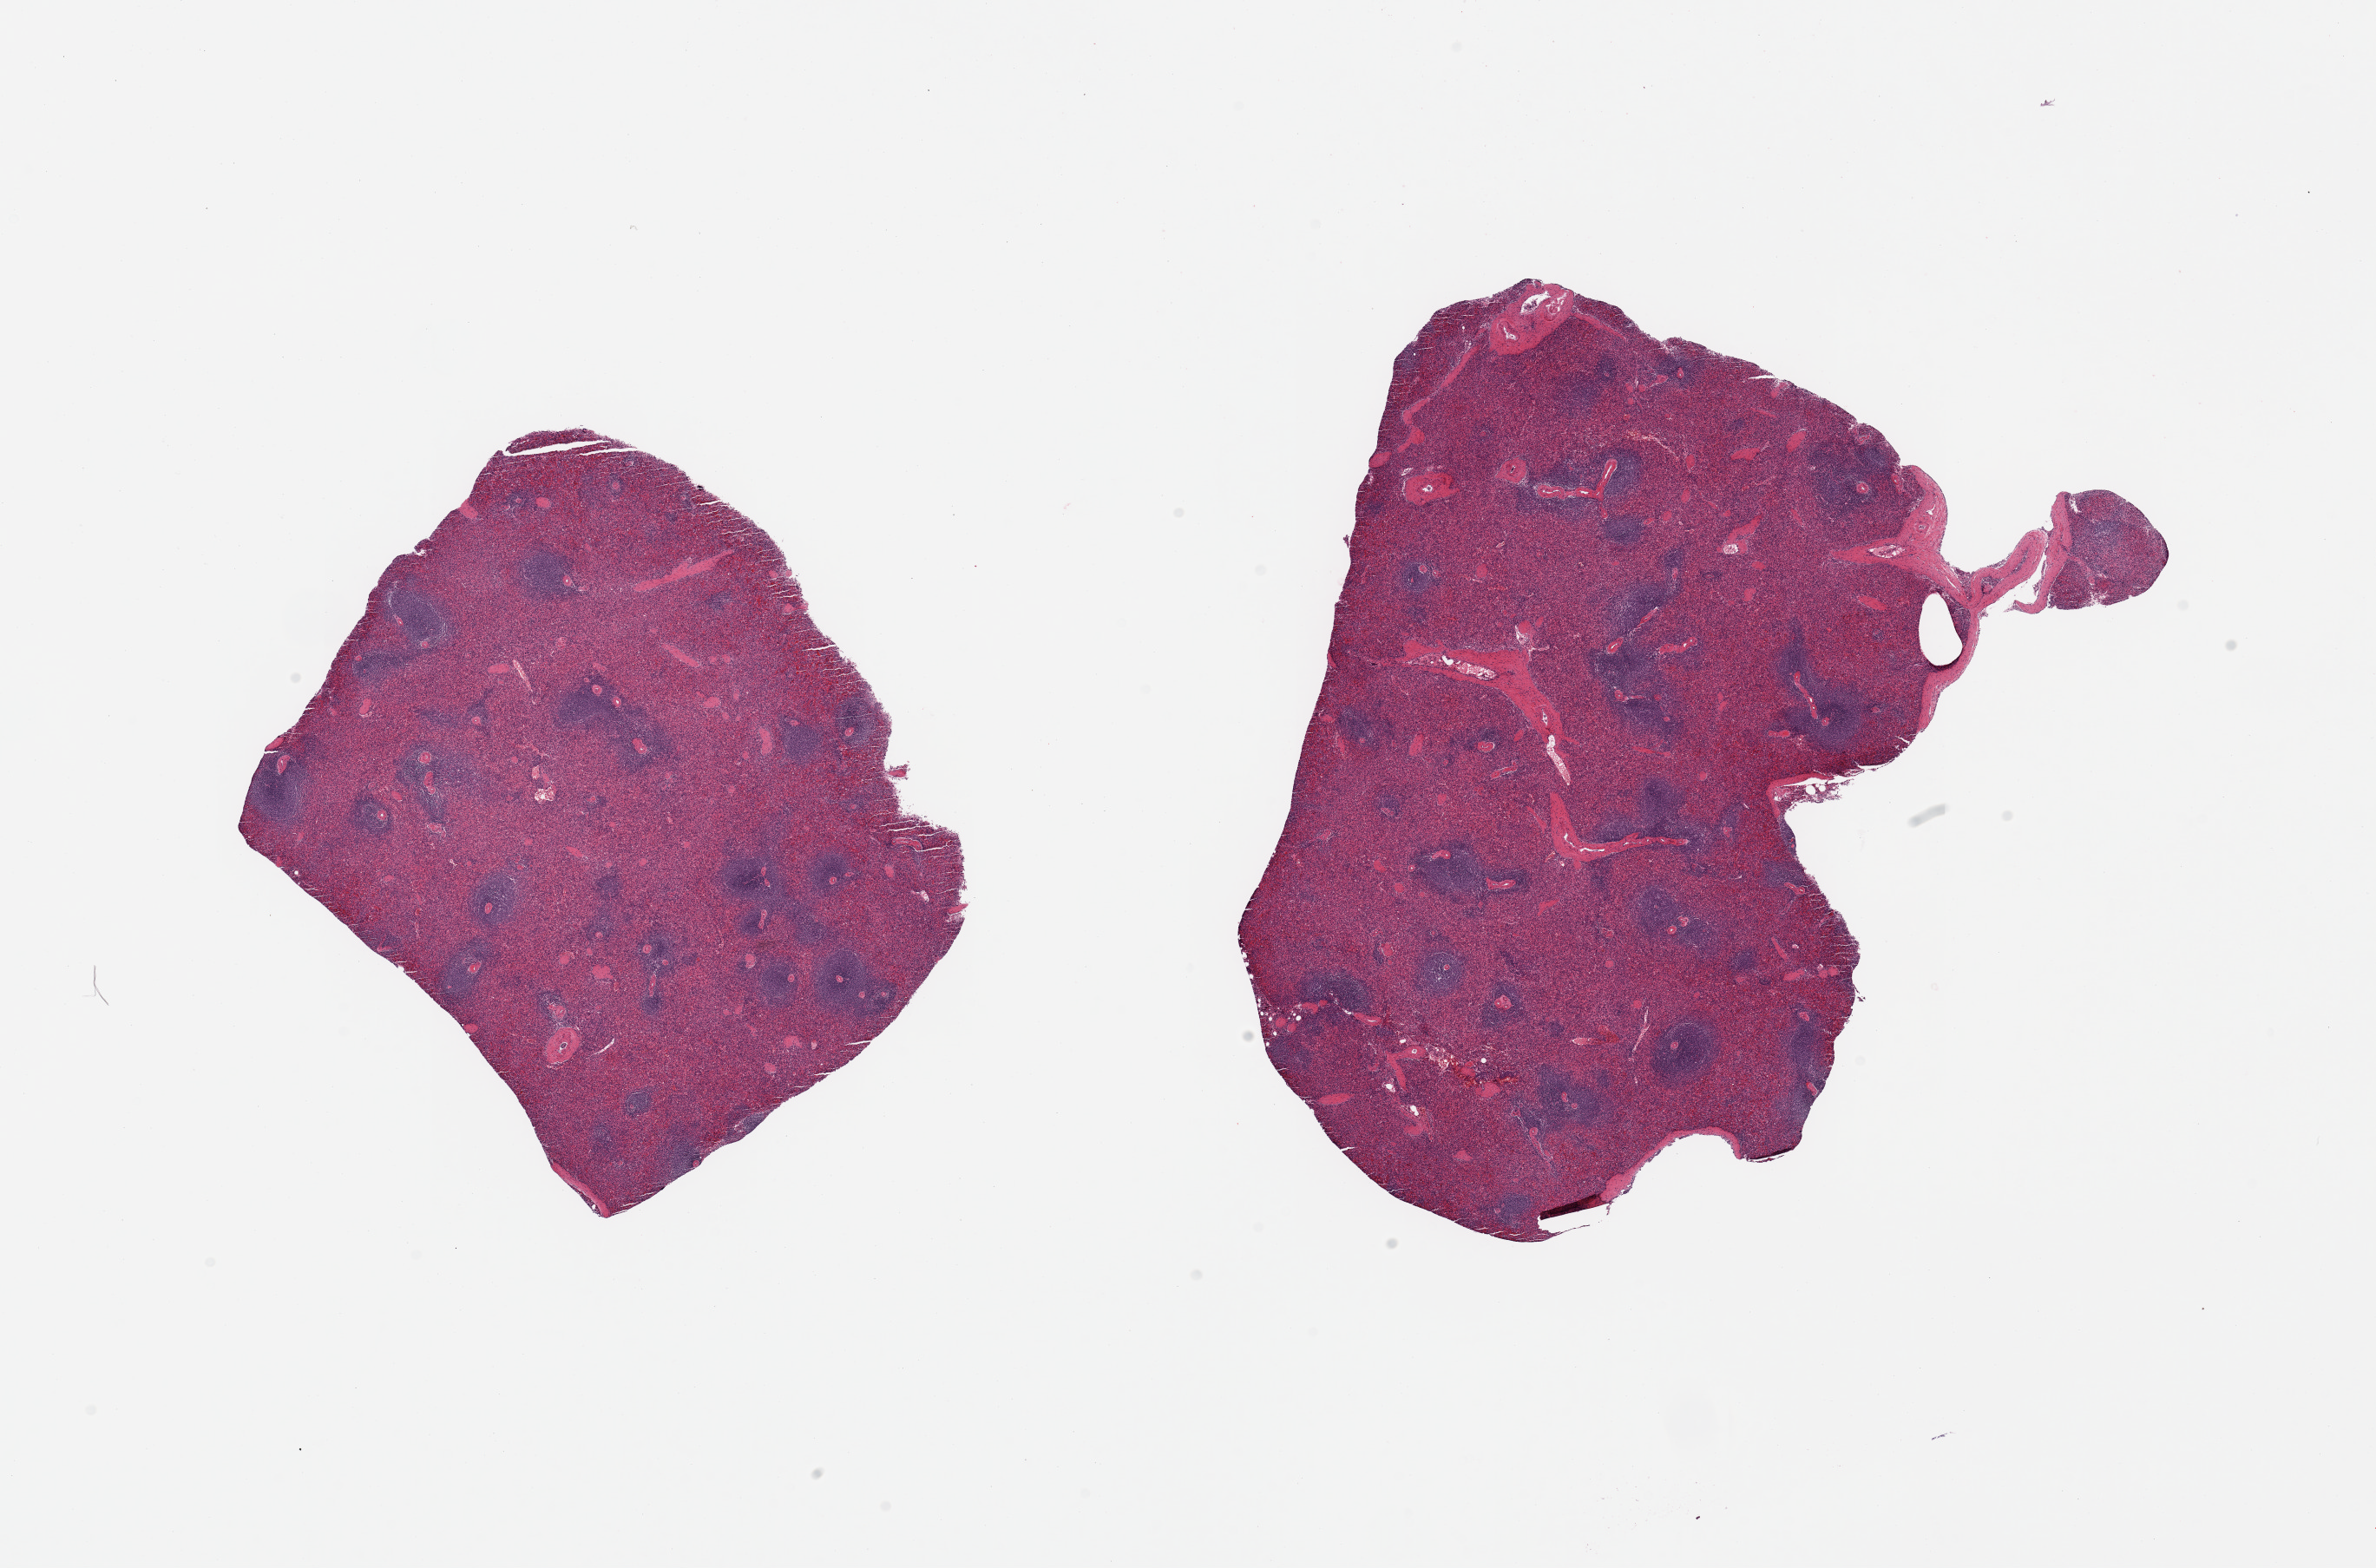
Digitized haematoxylin and eosin-stained section, brightfield, shown as a low-resolution overview of the whole scanned area (about 21.7 x 14.3 mm). PAXgene-fixed, paraffin-embedded tissue. Target tissue: spleen. Tissue donor sample. Donor: female.
Review note (as recorded): 2 pieces.